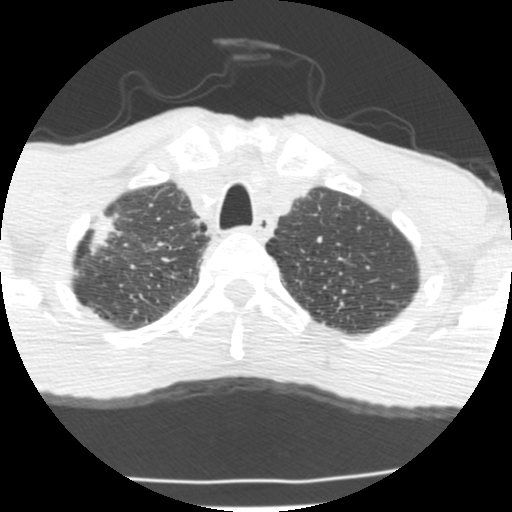
Low-dose screening chest CT, axial slice; second screening round (one year after baseline); lung window (W 1500 / L -600 HU); 2.5 mm slice thickness; 120 kVp; slice 32 of 214 in the series. Male participant, aged 62 years at enrolment.
• Expert-annotated lung lesion, bounding box <66,214,137,273> (left, top, right, bottom; pixels).
• Reader record for this screening exam (exam-level; its link to the box is not recorded): non-calcified nodule or mass ≥4 mm, right upper lobe, 23 × 11 mm, spiculated (stellate) margins, soft tissue attenuation, pre-existing on the prior screen: yes.
• Official screen result: positive, change unspecified: nodule(s) >= 4 mm or enlarging nodule(s), mass(es), or other non-specific abnormalities suspicious for lung cancer.
• Participant outcome: lung cancer diagnosed 277 days after this screen — adenocarcinoma, NOS, right upper lobe, poorly differentiated (G3), stage IIA (AJCC 6th edition), 22 mm at pathology.